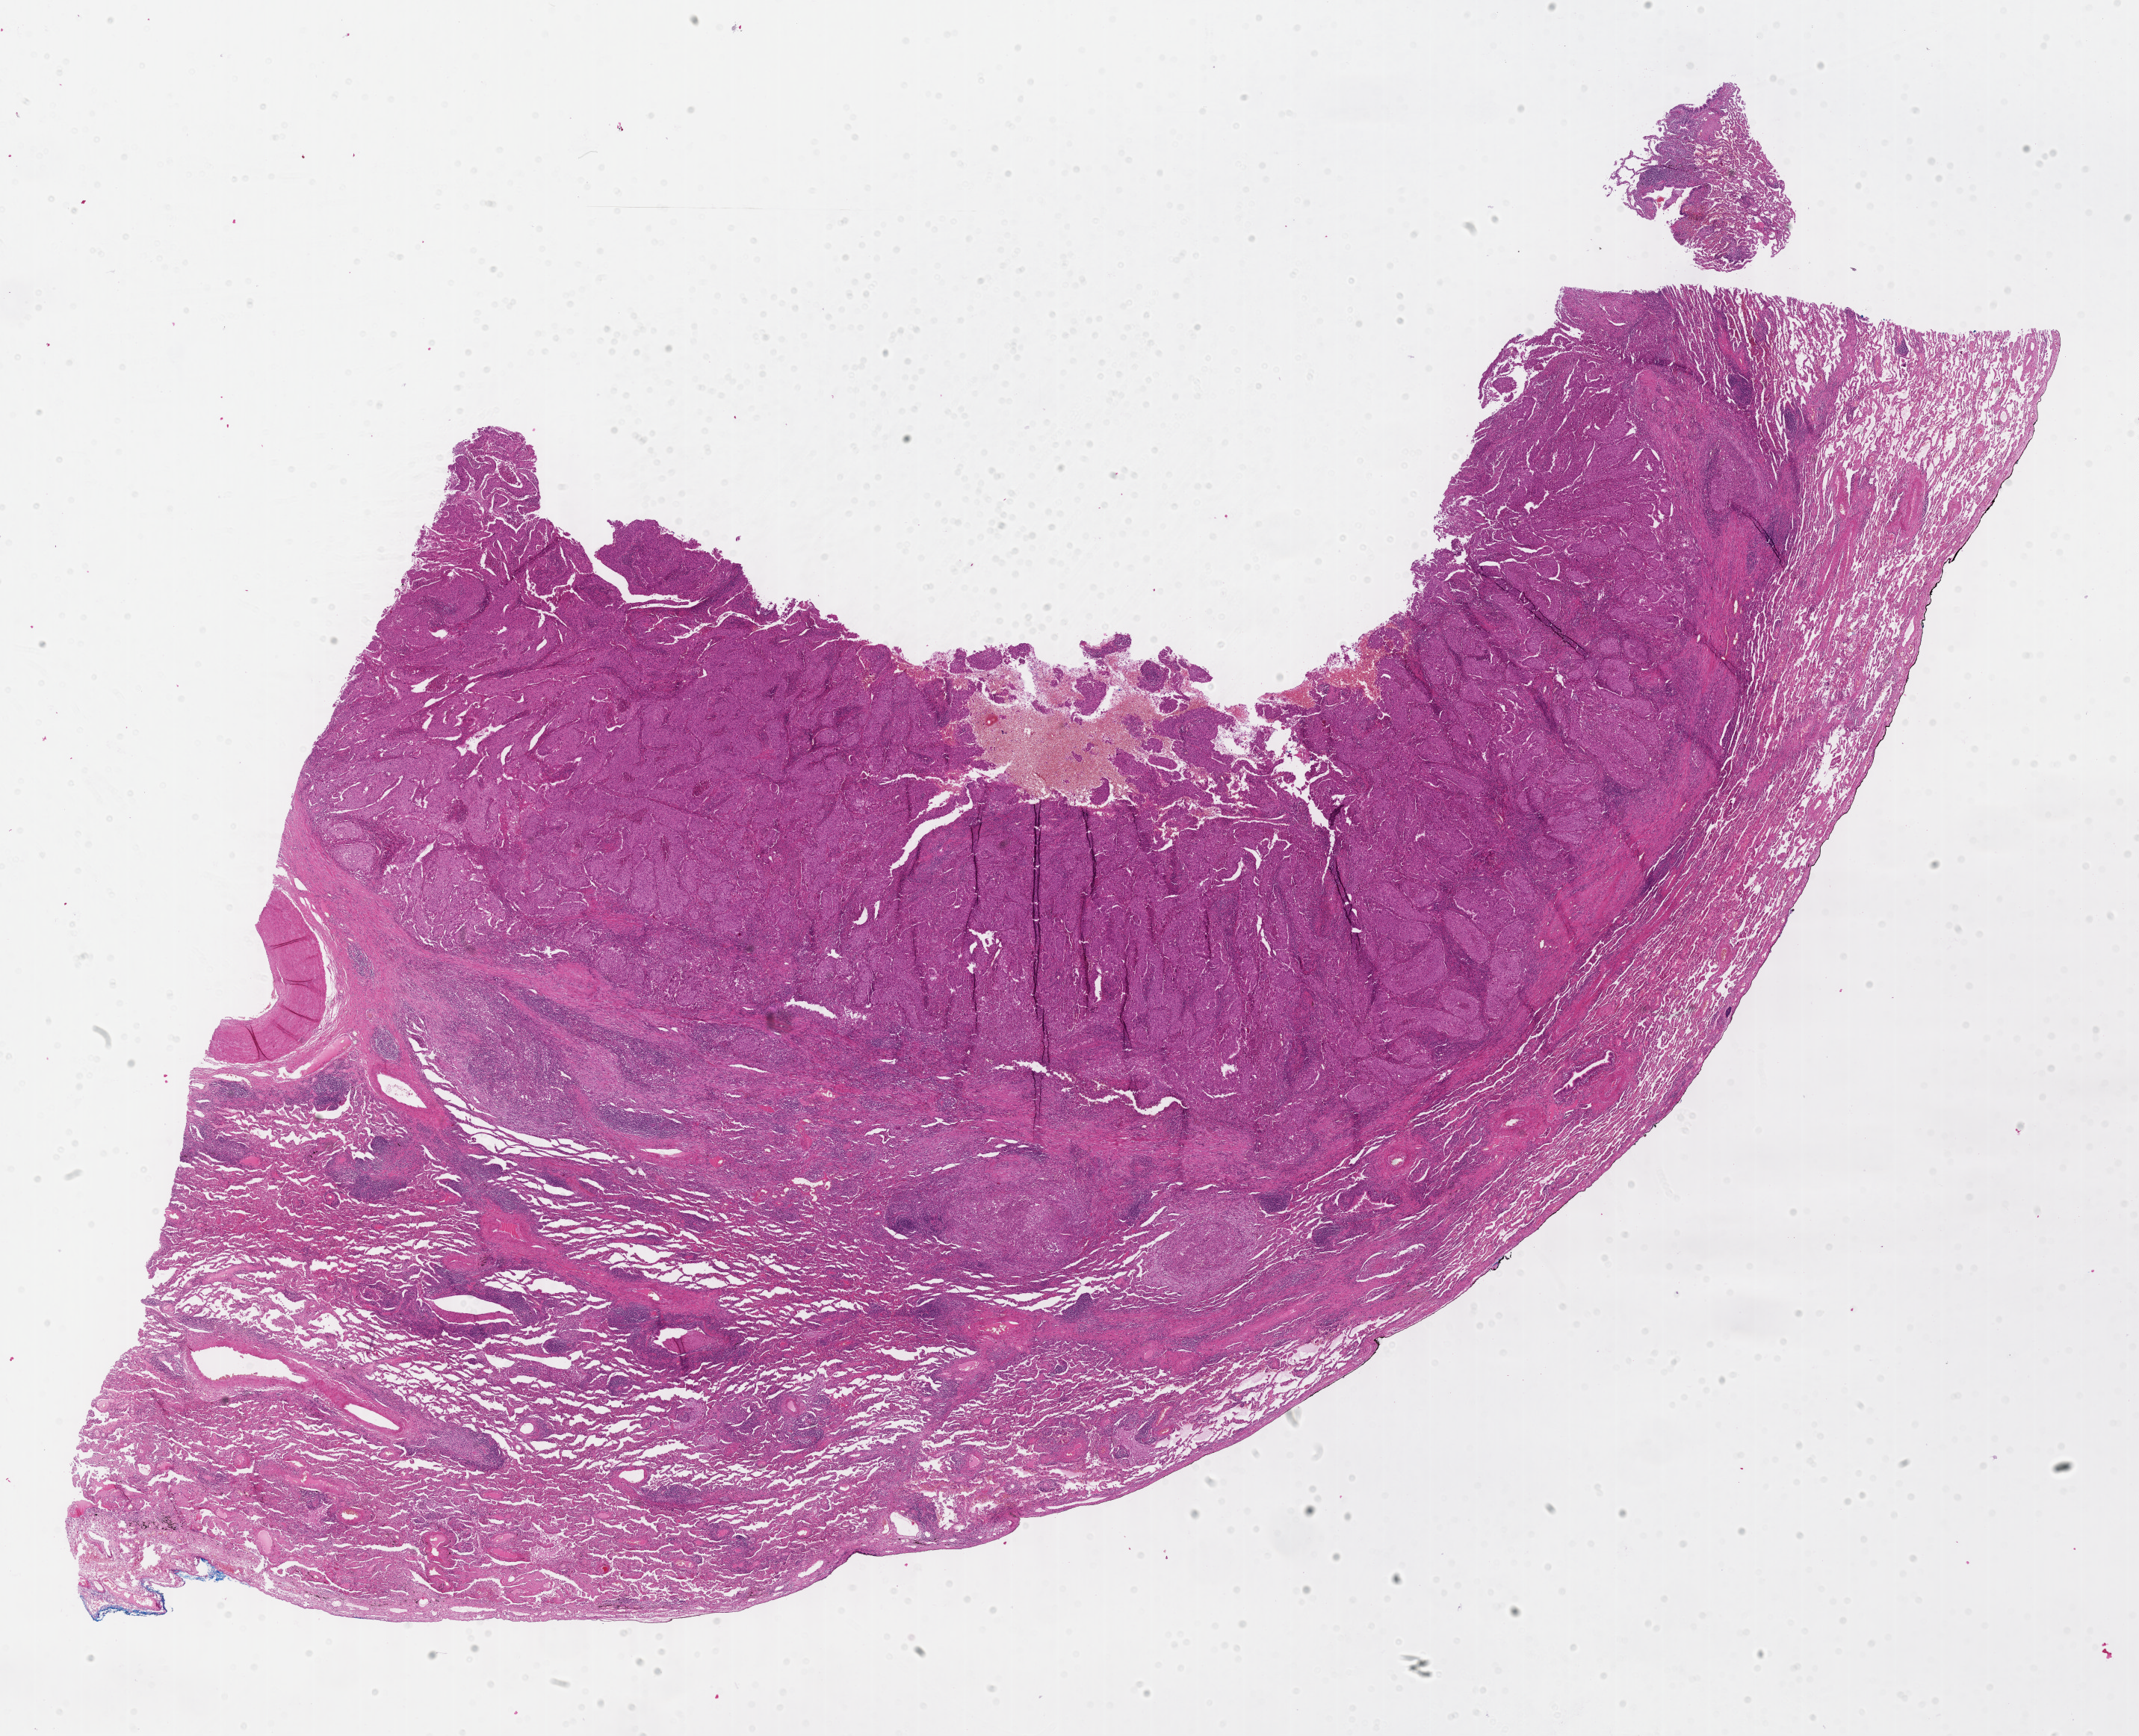
Whole-slide histology image, H&E-stained, whole scanned area (about 23.1 x 18.8 mm) shown as a low-resolution overview; formalin-fixed paraffin-embedded (FFPE) diagnostic section; lung, primary tumour sample. Male patient; age at initial diagnosis 60 years.
Histologic diagnosis: Squamous cell carcinoma, NOS (upper lobe, lung). Laterality: left. AJCC pathologic stage: IIB (6th edition).